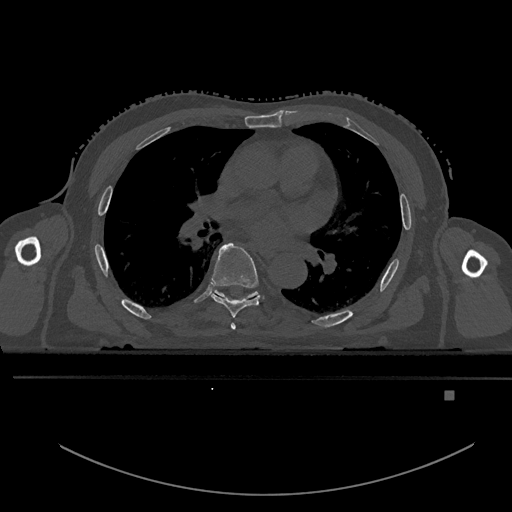
CT including the spine, one axial slice. Slice 298 of 969 in the series (ordered by position). Bone window (W 1800 / L 400 HU). 0.5 mm slice thickness. 512 × 512 image matrix. Patient: male, 82 years. Case-level facts recorded for this patient, not image findings: primary cancer: prostate; vertebrae with lytic lesions (as recorded): T11, T9, T8, T2.
Structures marked on this image (semi-automatically segmented with operator editing):
- T5 vertebra: bounding box <231,323,236,330> (left, top, right, bottom; pixels)
- T6 vertebra: <211,242,260,318>
- T7 vertebra: <215,291,256,298>